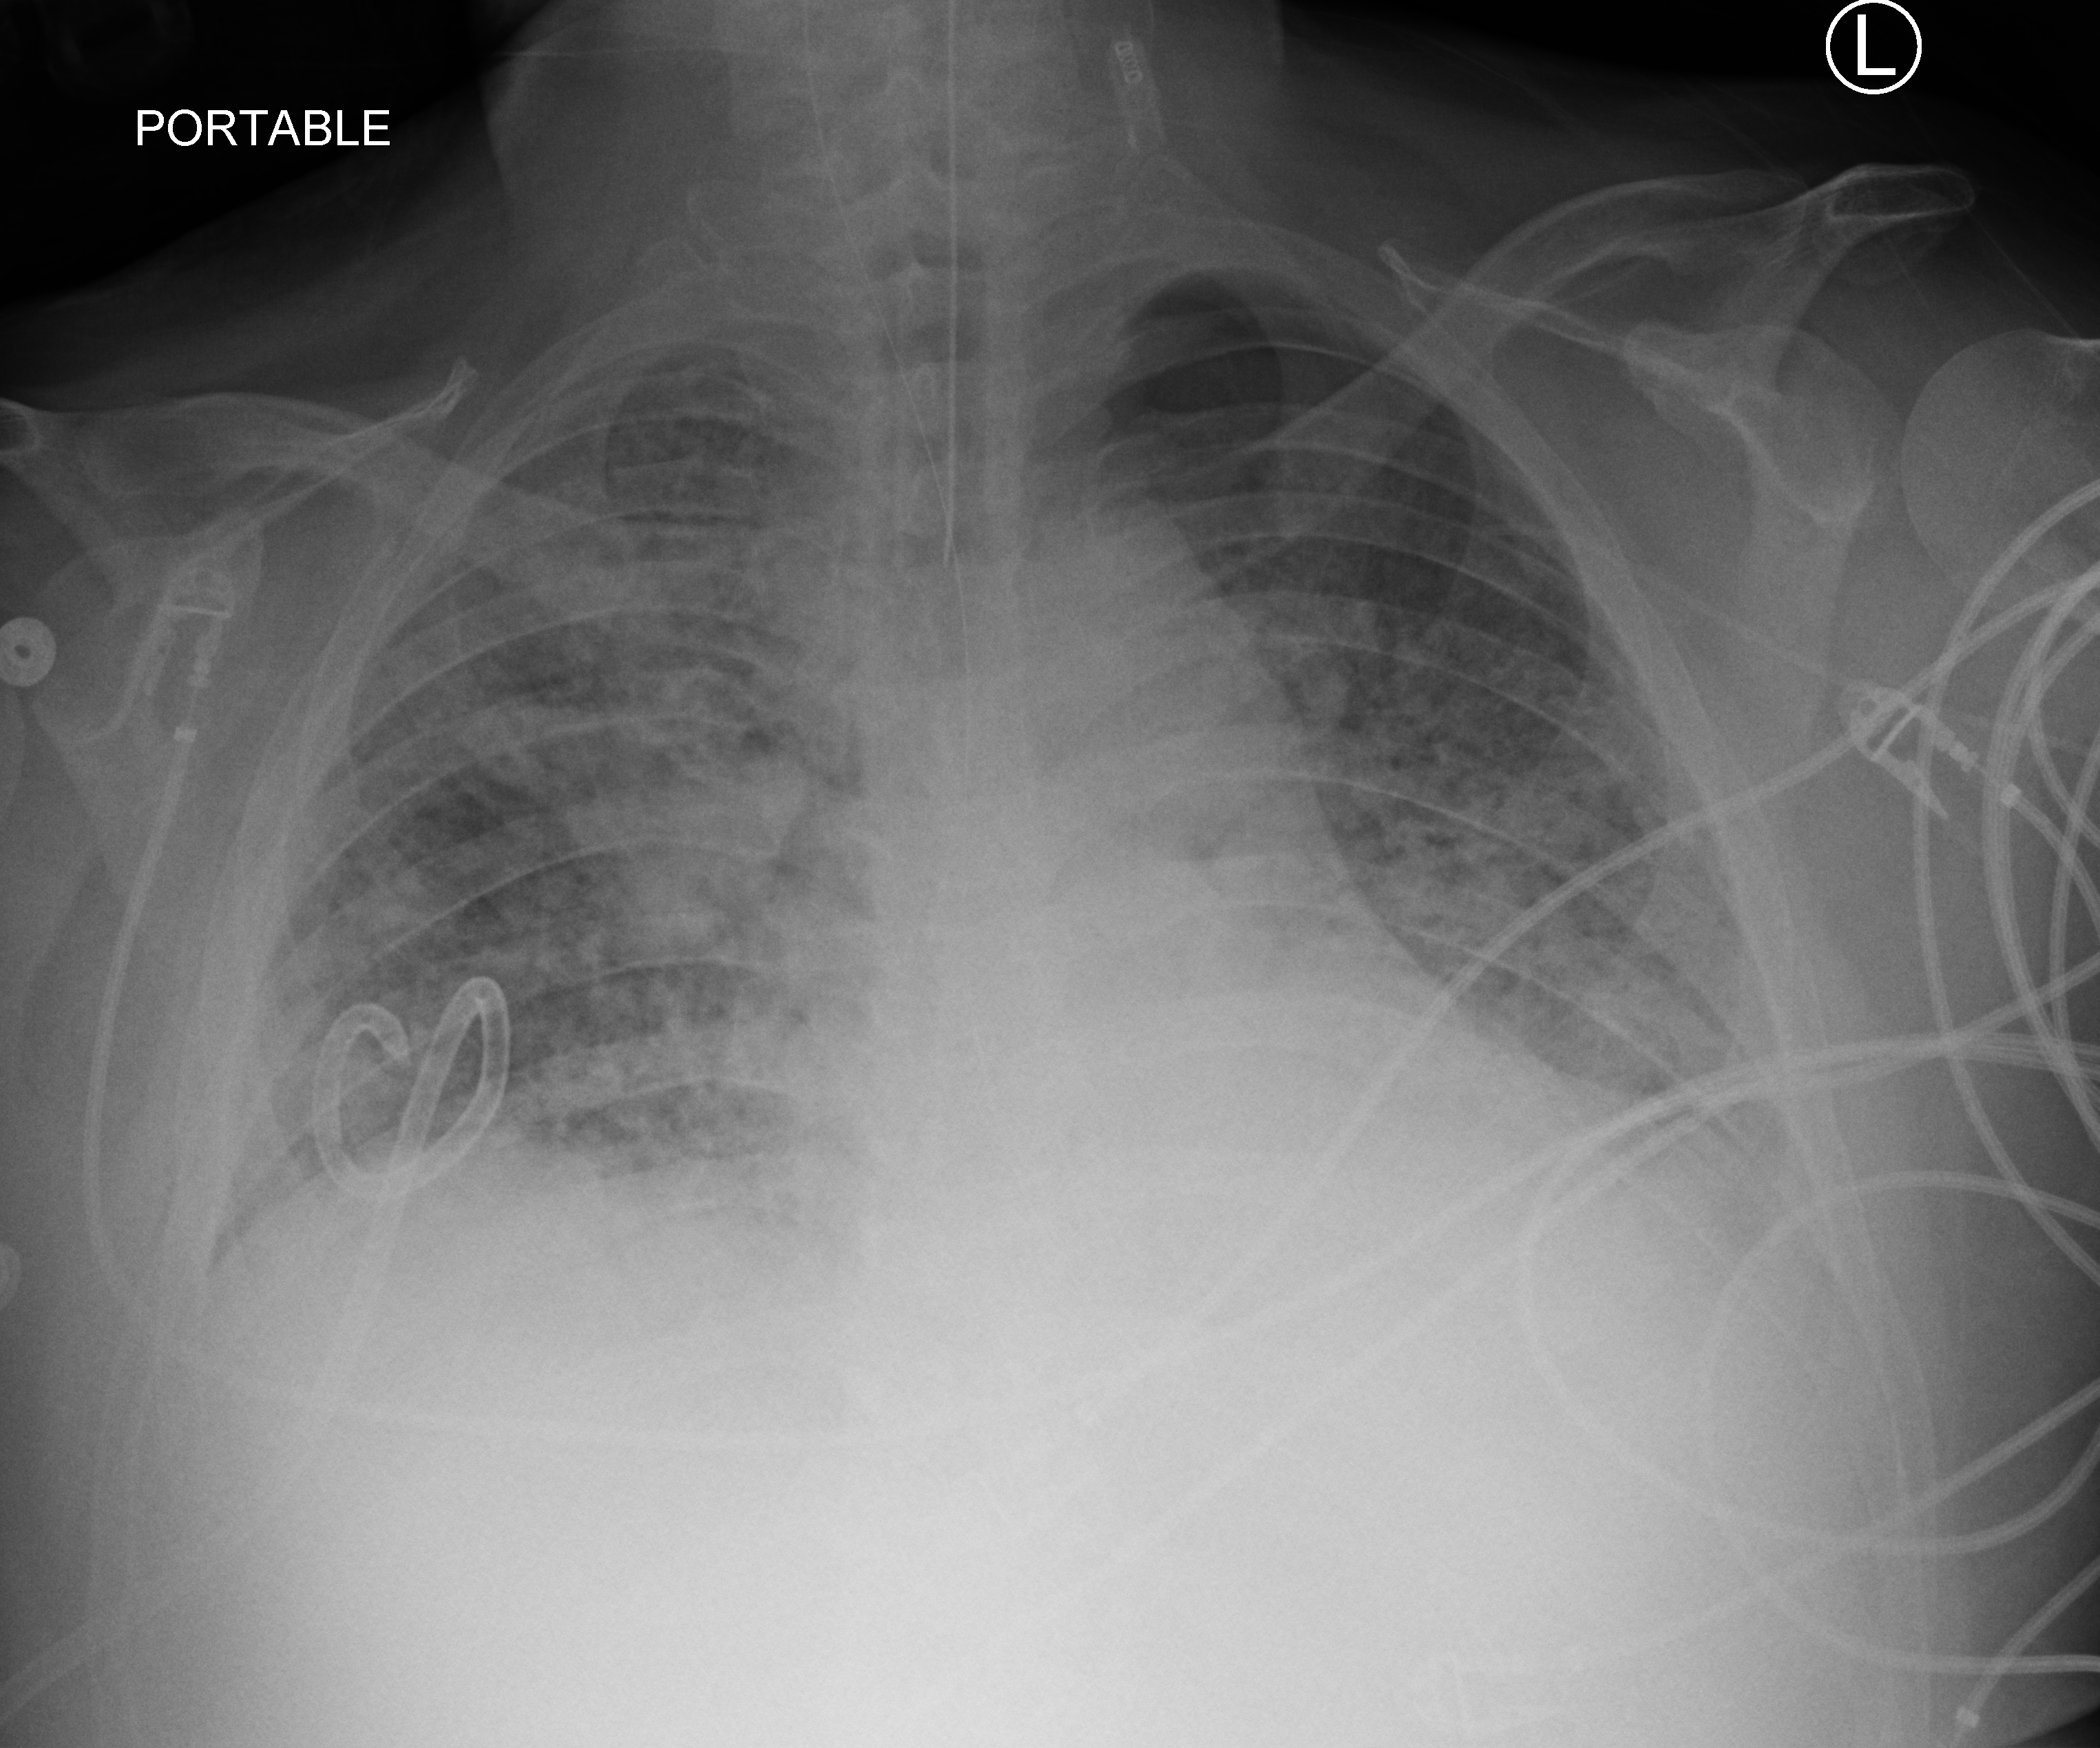
Chest X-ray (portable), anteroposterior (AP) projection. Patient hospitalised with COVID-19, aged 18–59 years.
Admission-level facts for this patient (not findings on this image; timing relative to this image not recorded): mechanically ventilated during this hospital stay: yes.